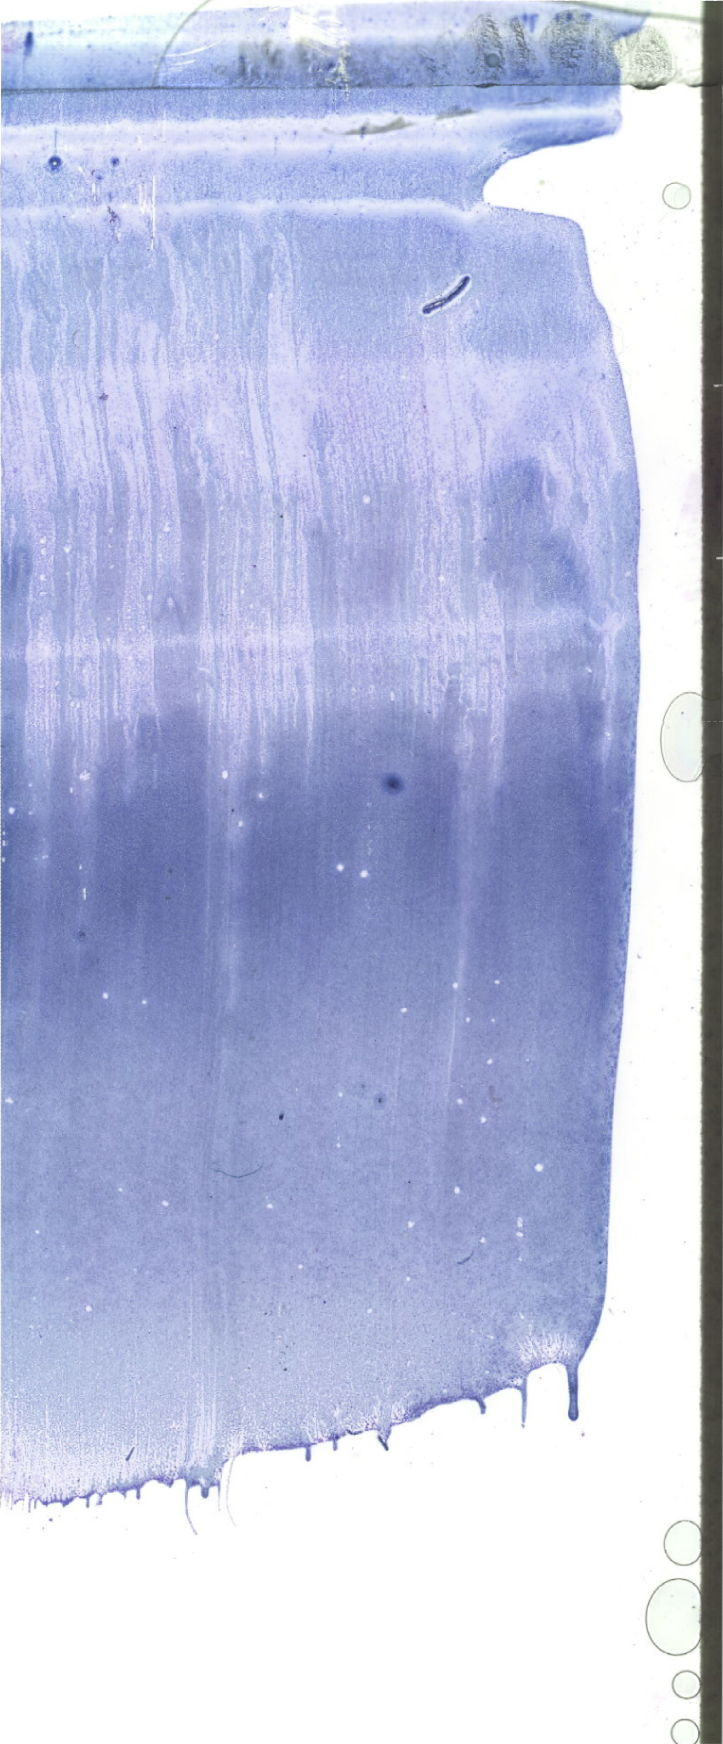
May-Grünwald-Giemsa (MGG)-stained marrow aspirate smear (whole slide), whole scanned area (about 20.5 x 49.4 mm) shown as a low-resolution overview. Female patient.
- diagnosis: Acute Myeloid Leukemia with Minimal Differentiation